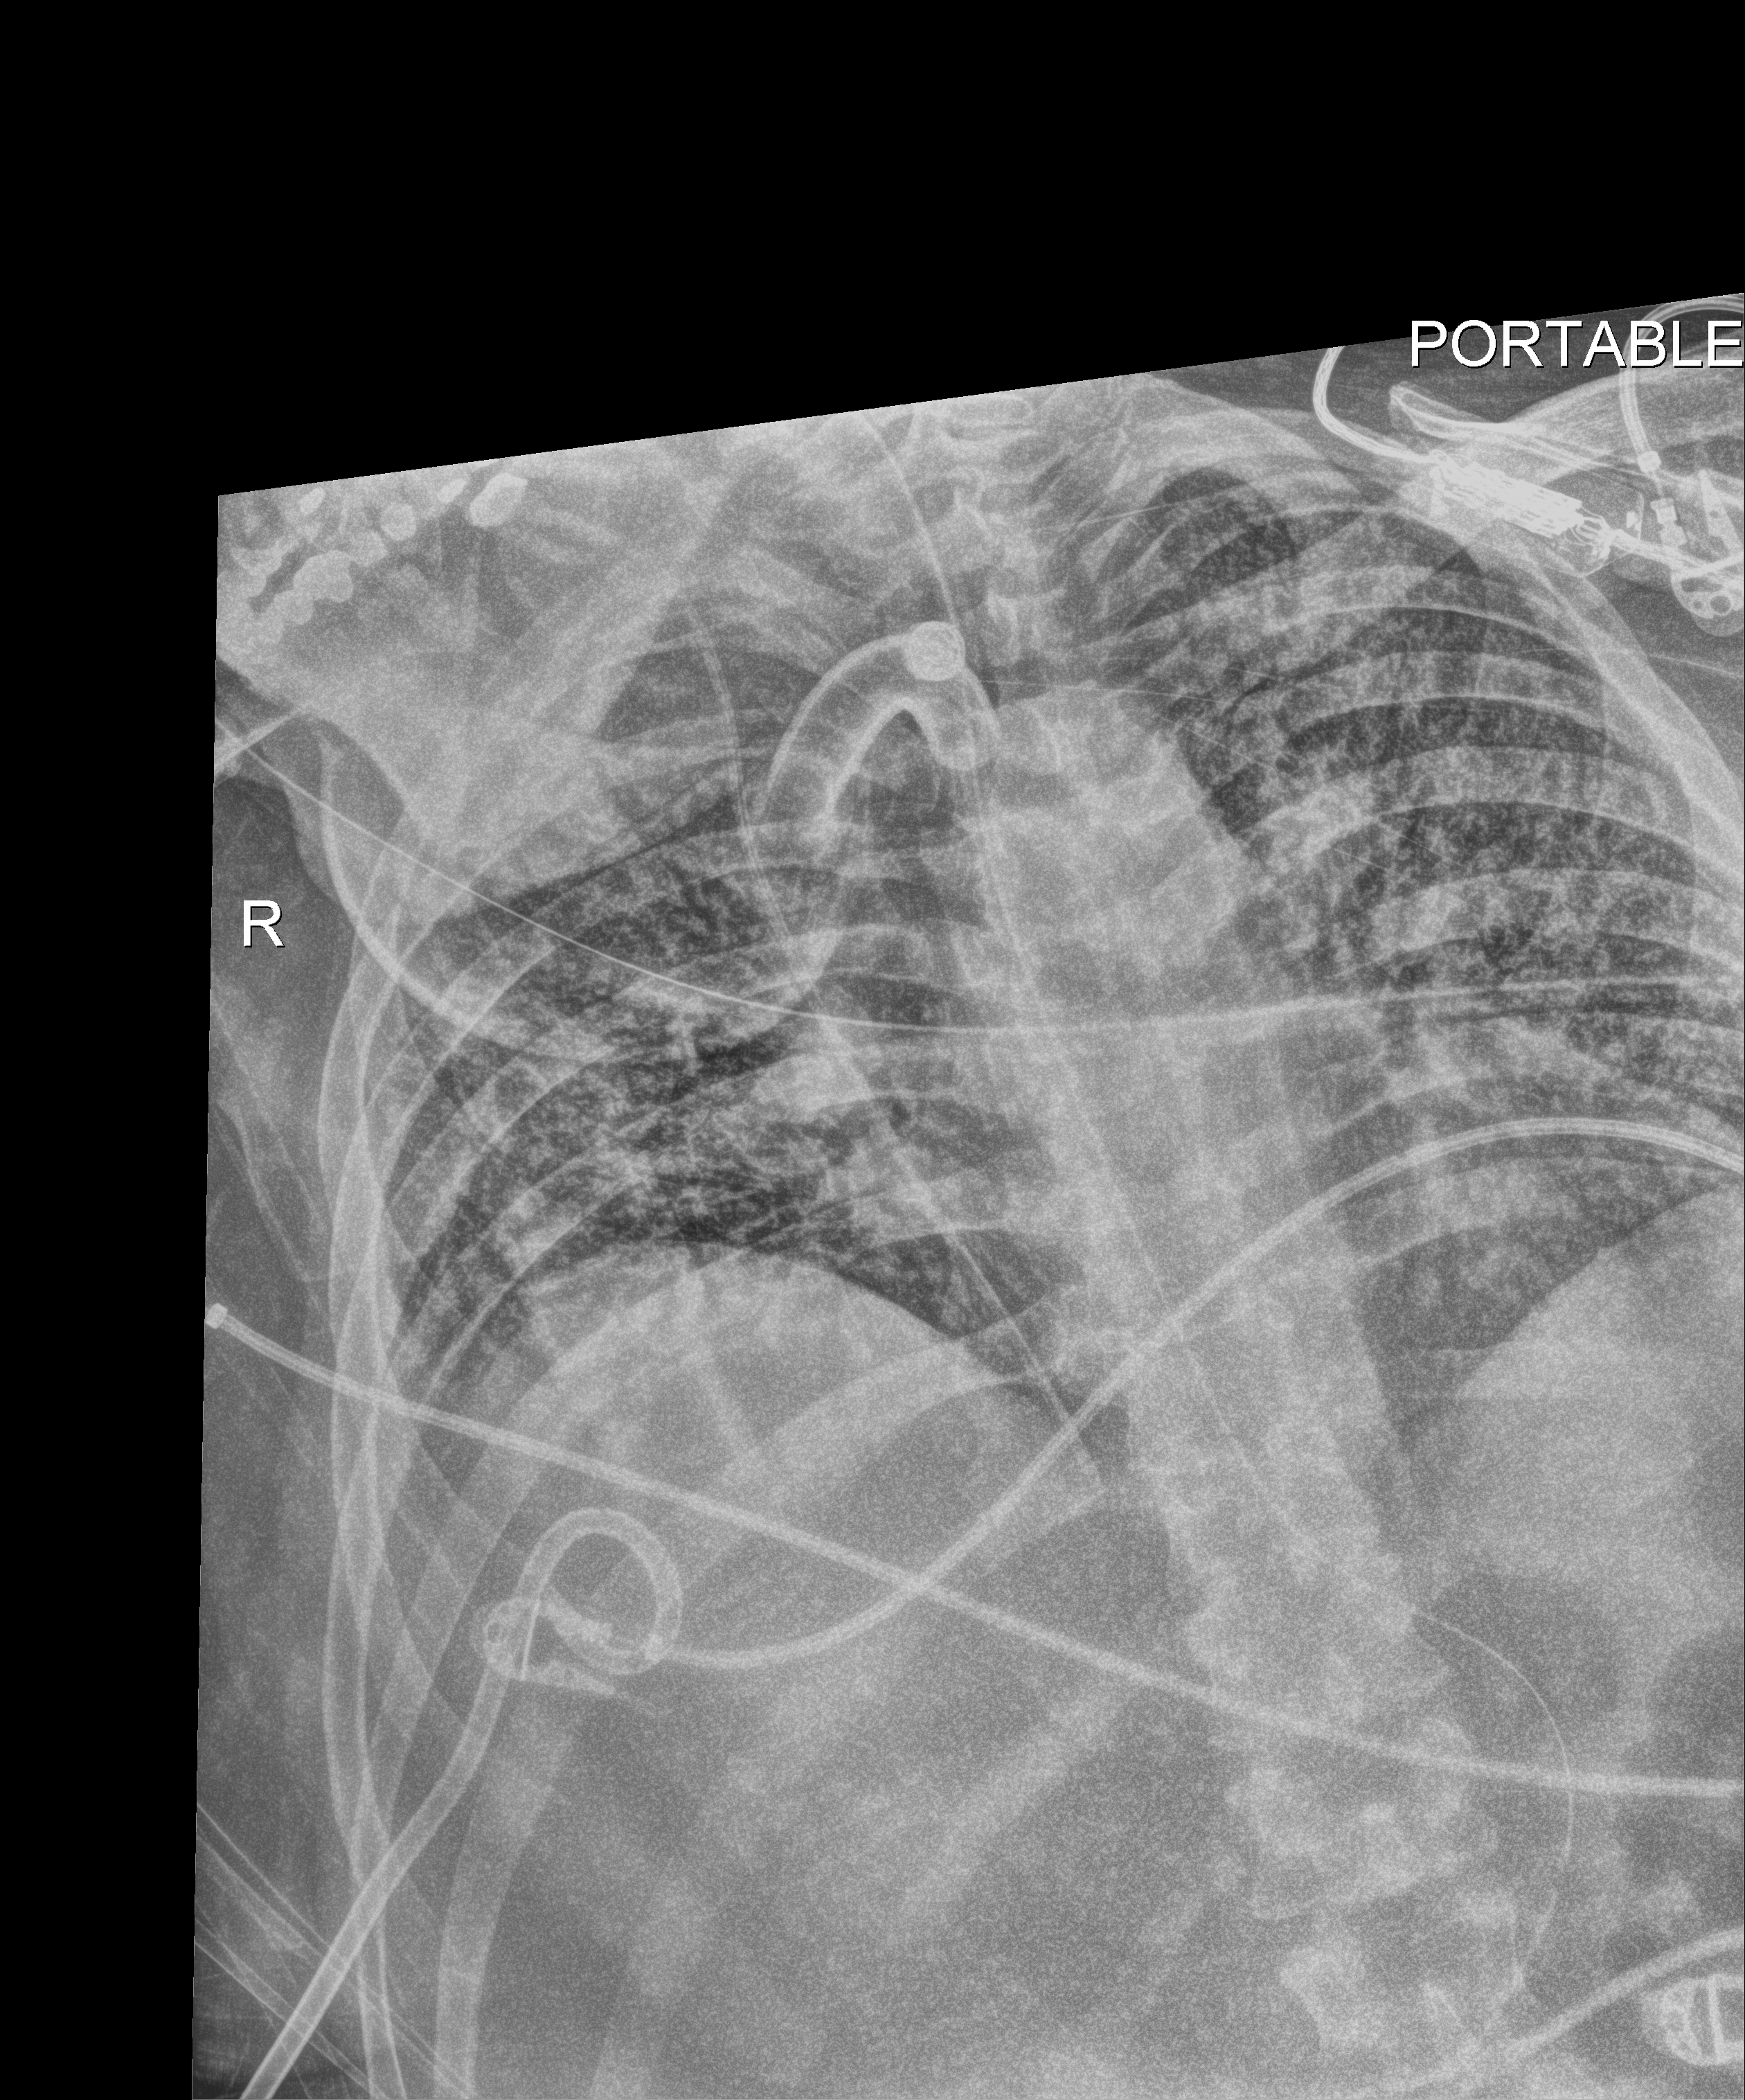
Portable chest radiograph; anteroposterior (AP) projection. Male patient hospitalised with COVID-19, age 18–59 years.
Admission-level facts for this patient (not findings on this image; timing relative to this image not recorded): length of hospital stay: 80 days; admitted to intensive care during this hospital stay: yes; mechanically ventilated during this hospital stay: yes.